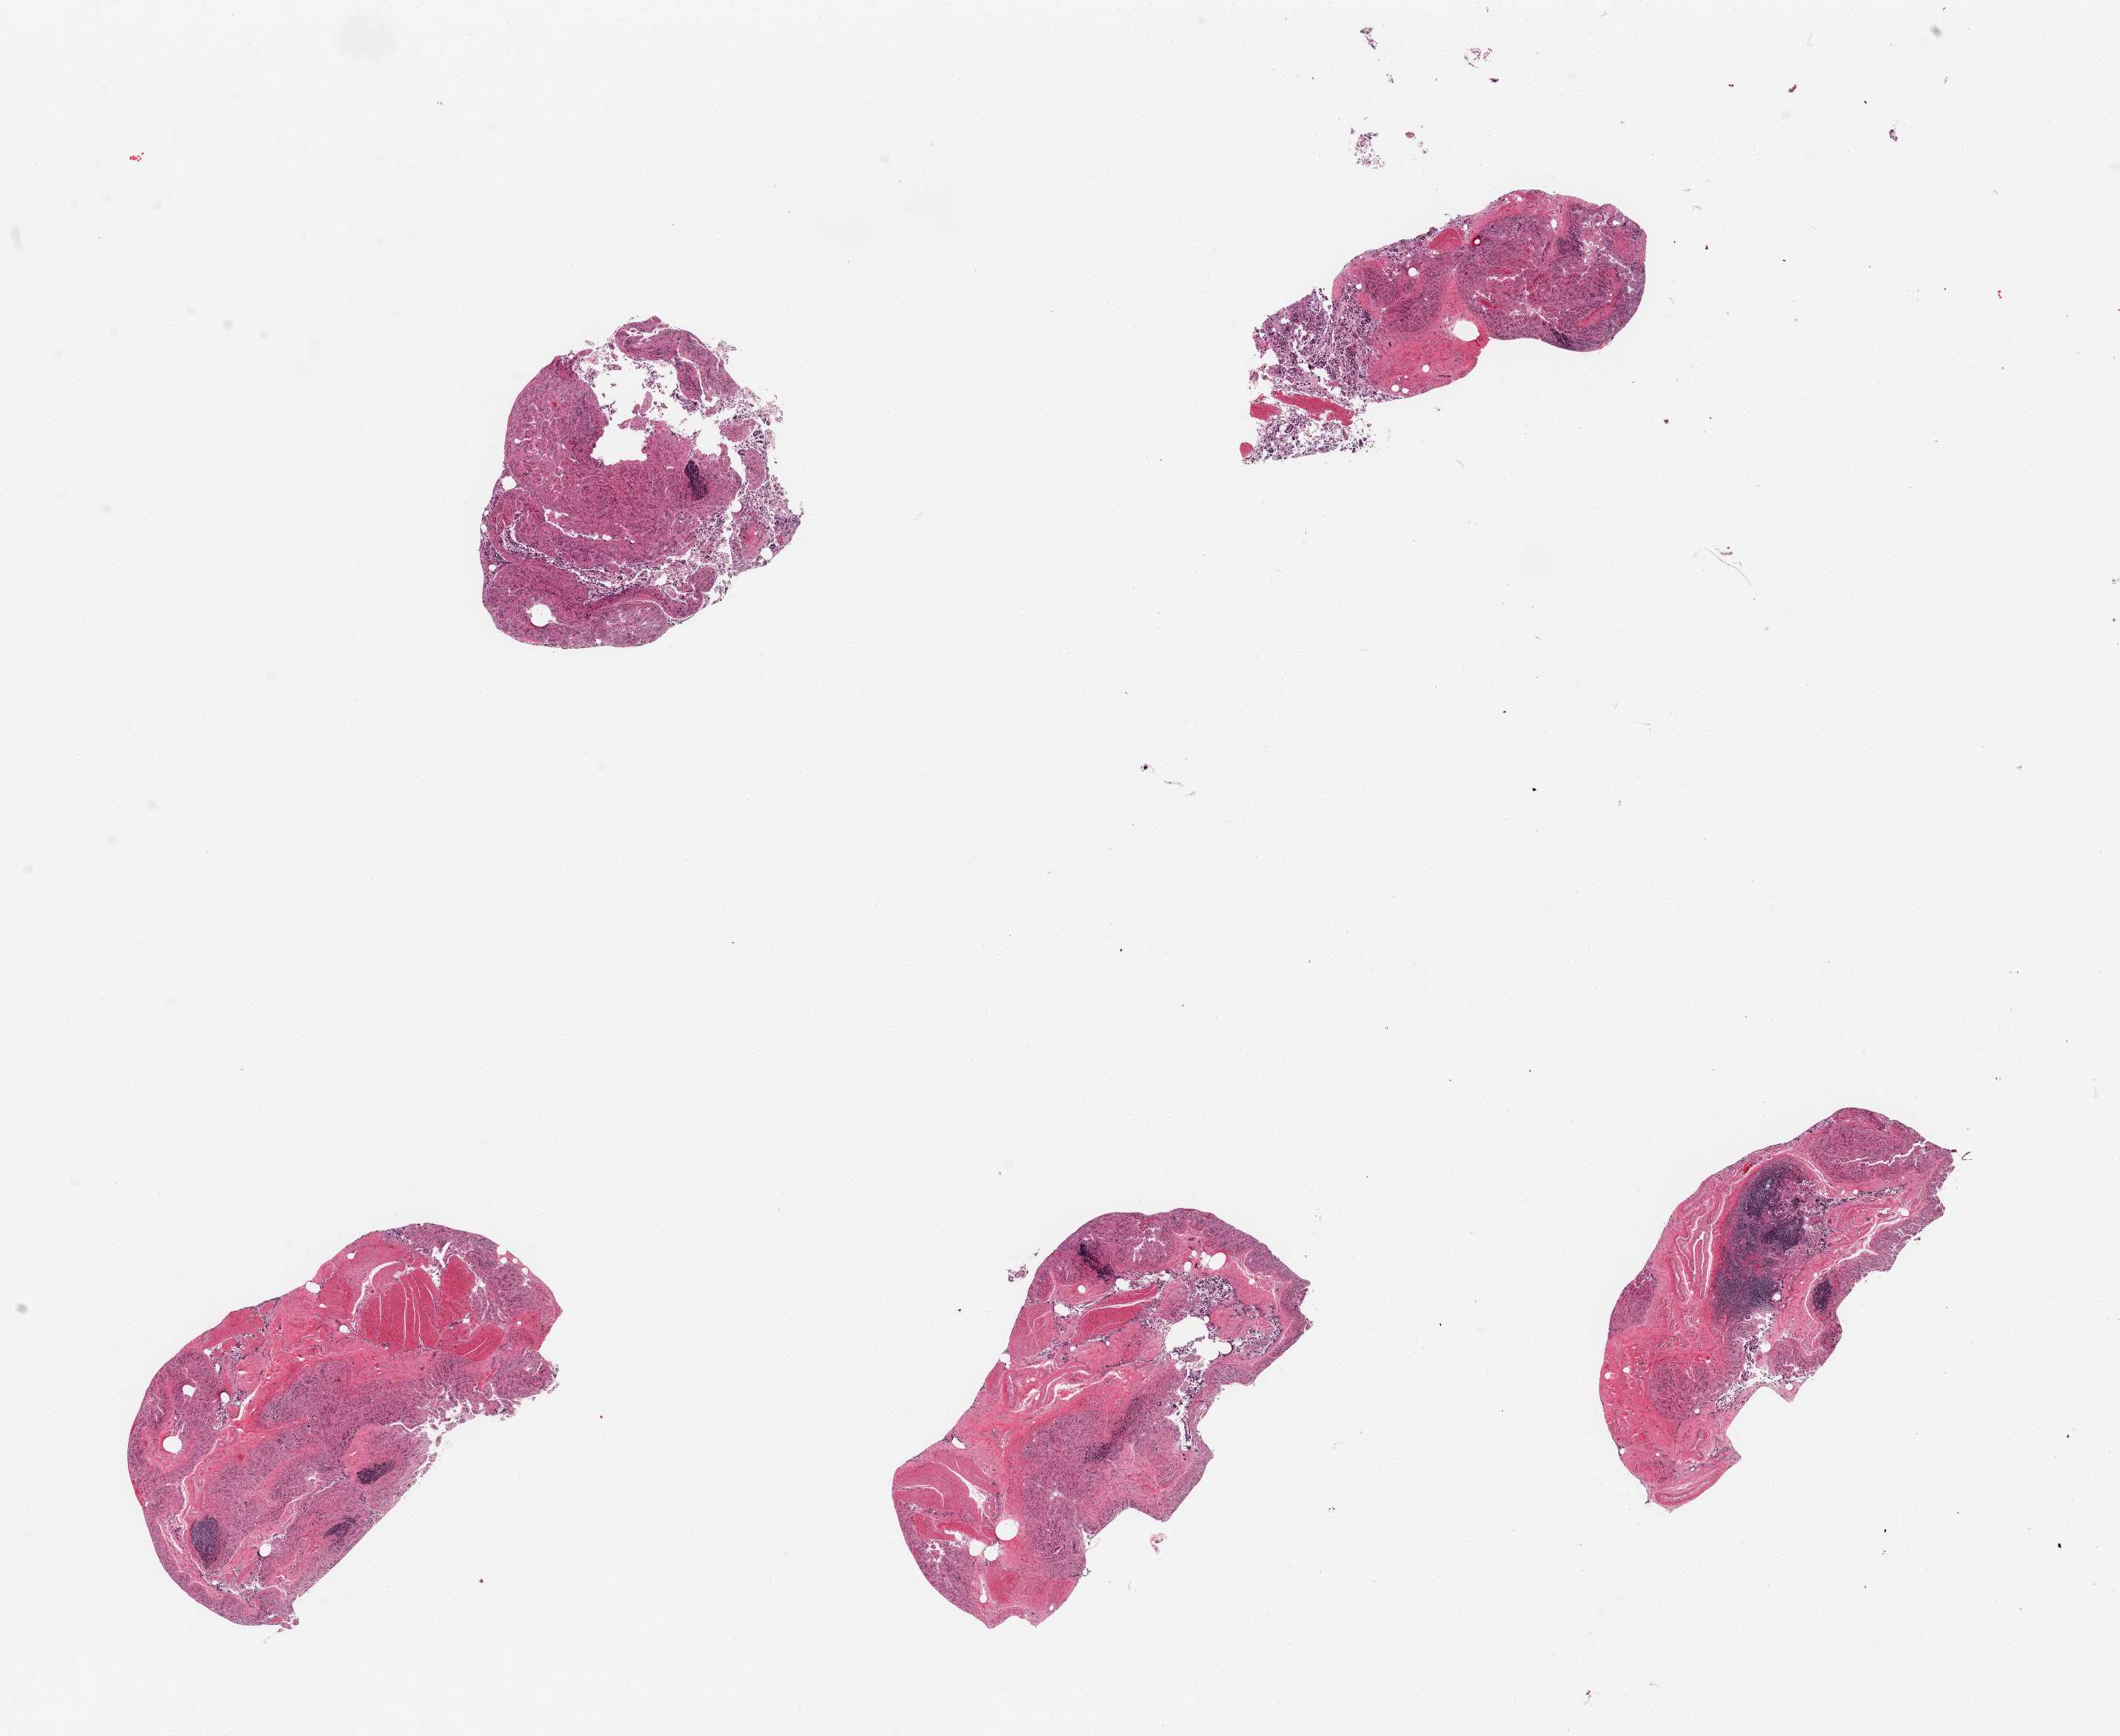
Whole-slide image, hematoxylin and eosin (H&E) stain, brightfield, a low-resolution overview of the entire scanned area, about 22.6 x 18.5 mm; PAXgene-fixed paraffin-embedded (PFPE) section; sampled site (target tissue): ileum; donor tissue sample. Donor: male.
Reviewer comment on this tissue sample: 5 pieces, several small deposits of lymphoid tissue.